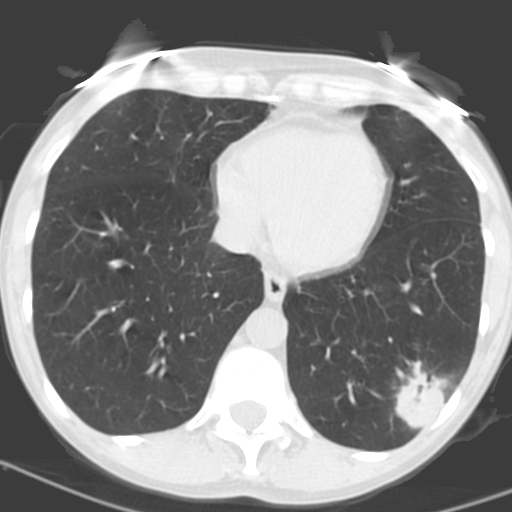
Low-dose screening chest CT, axial slice; baseline annual screen; lung window (W 1500 / L -600 HU); 3.2 mm slice thickness; 512 × 512 image matrix. Female, age 56 years at enrolment.
Expert reader's lesion annotation, bounding box [x1, y1, x2, y2] px = [381, 361, 460, 431]. The exam's reader record, not a measurement of the box and not confirmed to be the same lesion: non-calcified nodule or mass ≥4 mm, left lower lobe, 31 × 23 mm, poorly defined margins, soft tissue attenuation, pre-existing on the prior screen: no. Official screen result: positive, change unspecified: nodule(s) >= 4 mm or enlarging nodule(s), mass(es), or other non-specific abnormalities suspicious for lung cancer. Participant outcome: lung cancer diagnosed 27 days after this screen — squamous cell carcinoma, NOS, left lower lobe, poorly differentiated (G3), stage IB (AJCC 6th edition), 35 mm at pathology.